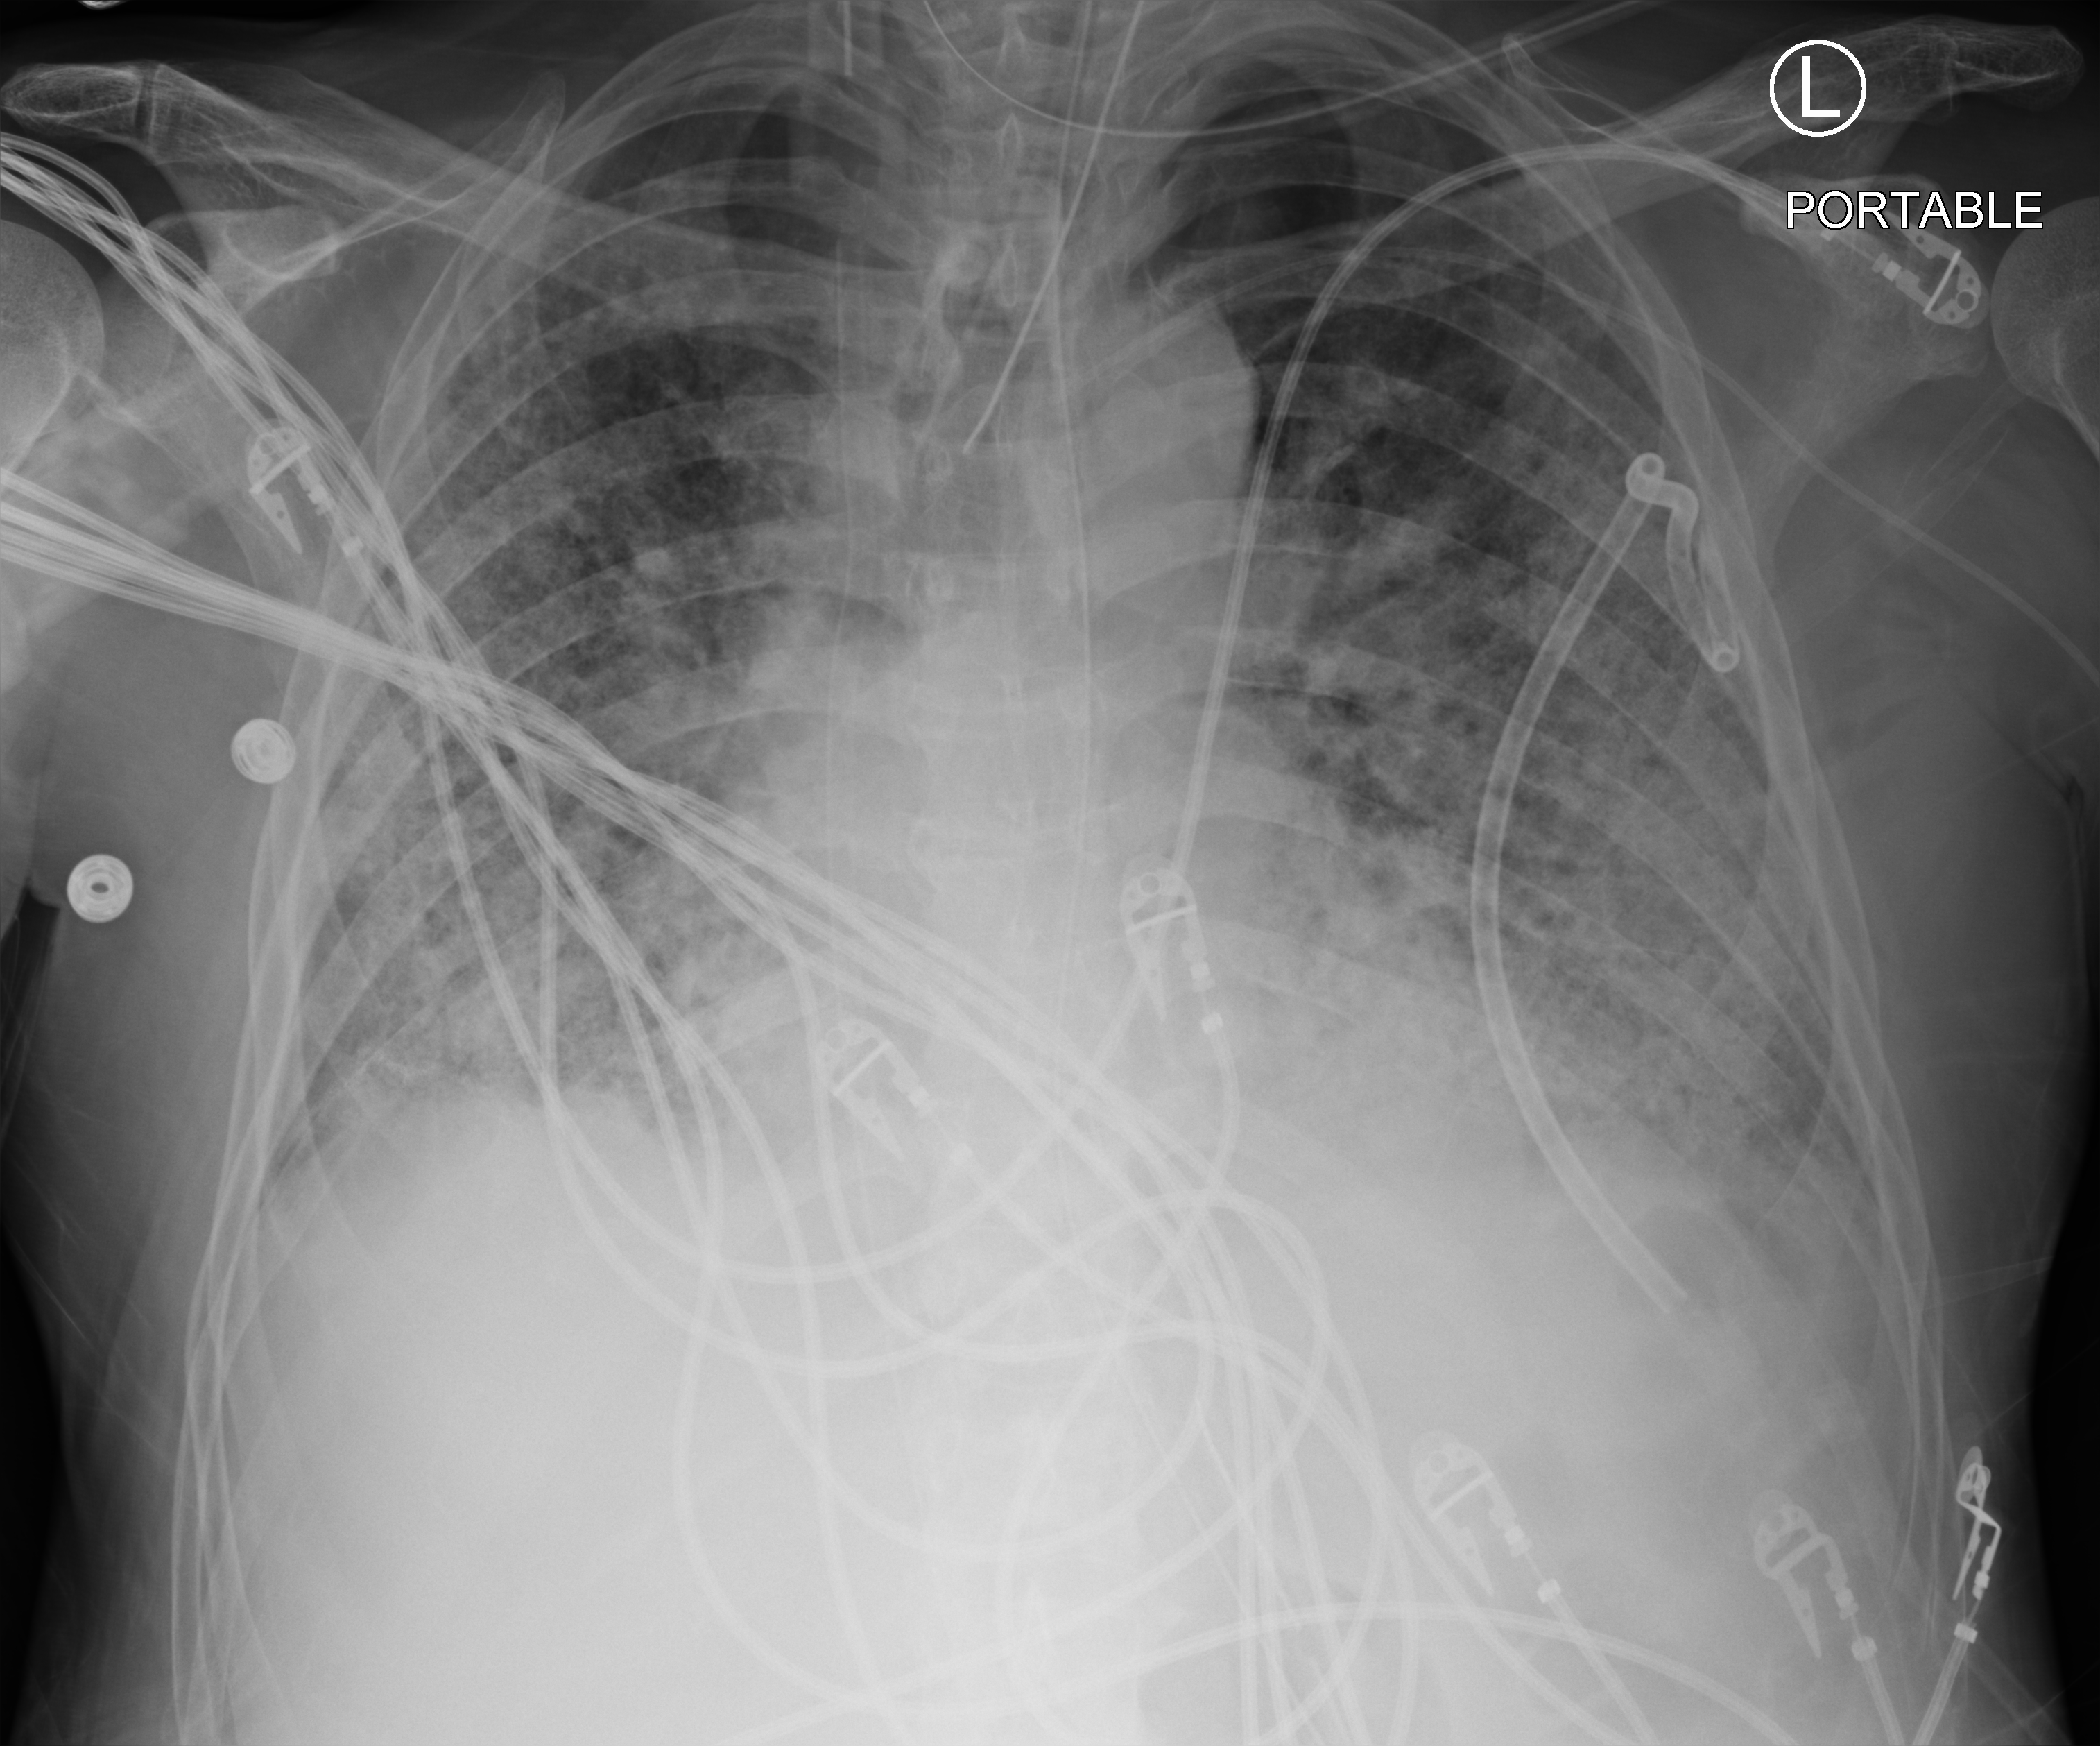
Chest X-ray (portable), anteroposterior (AP) projection. Male patient hospitalised with COVID-19, age 60–74 years.
Hospital-stay facts (about this admission, not read from this image; timing relative to this image not recorded): admitted to intensive care during this hospital stay: yes.